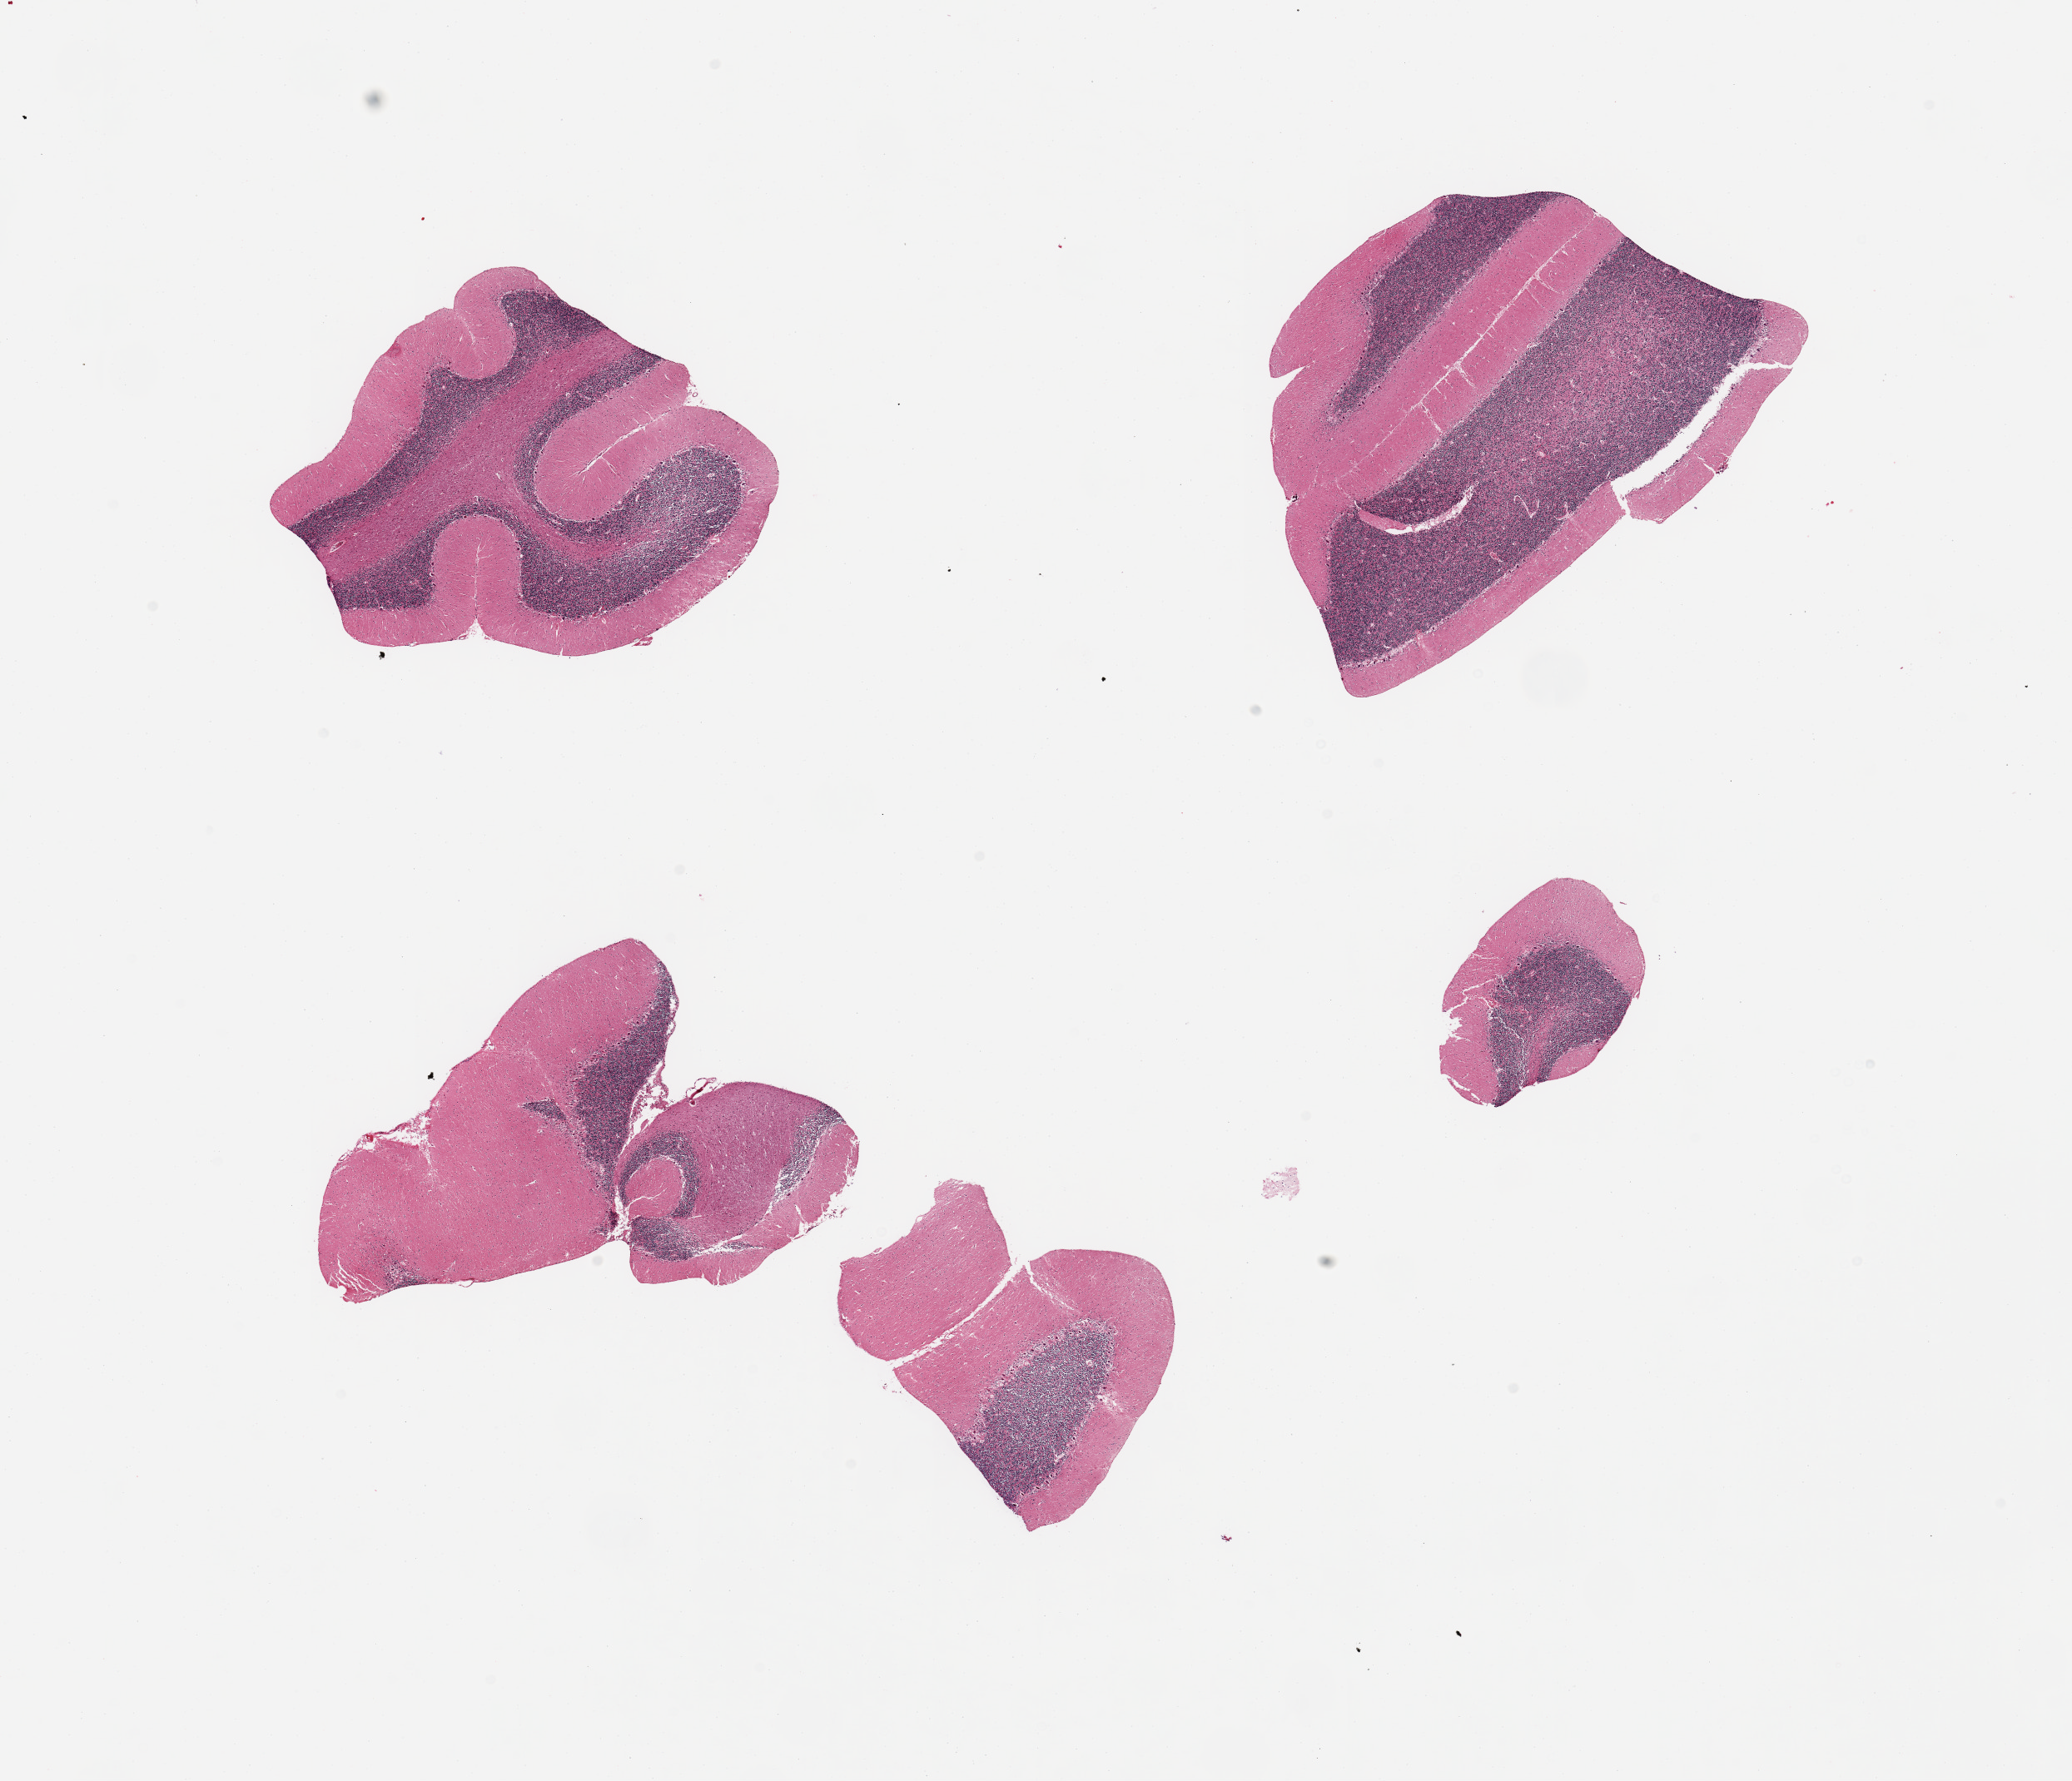
Digitized hematoxylin and eosin (H&E)-stained section, a low-resolution overview of the entire scanned area, about 19.7 x 16.9 mm. PAXgene-fixed, paraffin-embedded tissue. Section of cerebellum (target tissue). Tissue donor sample. Donor: male.
* reviewer comment on this tissue sample: 4 fragmented pieces